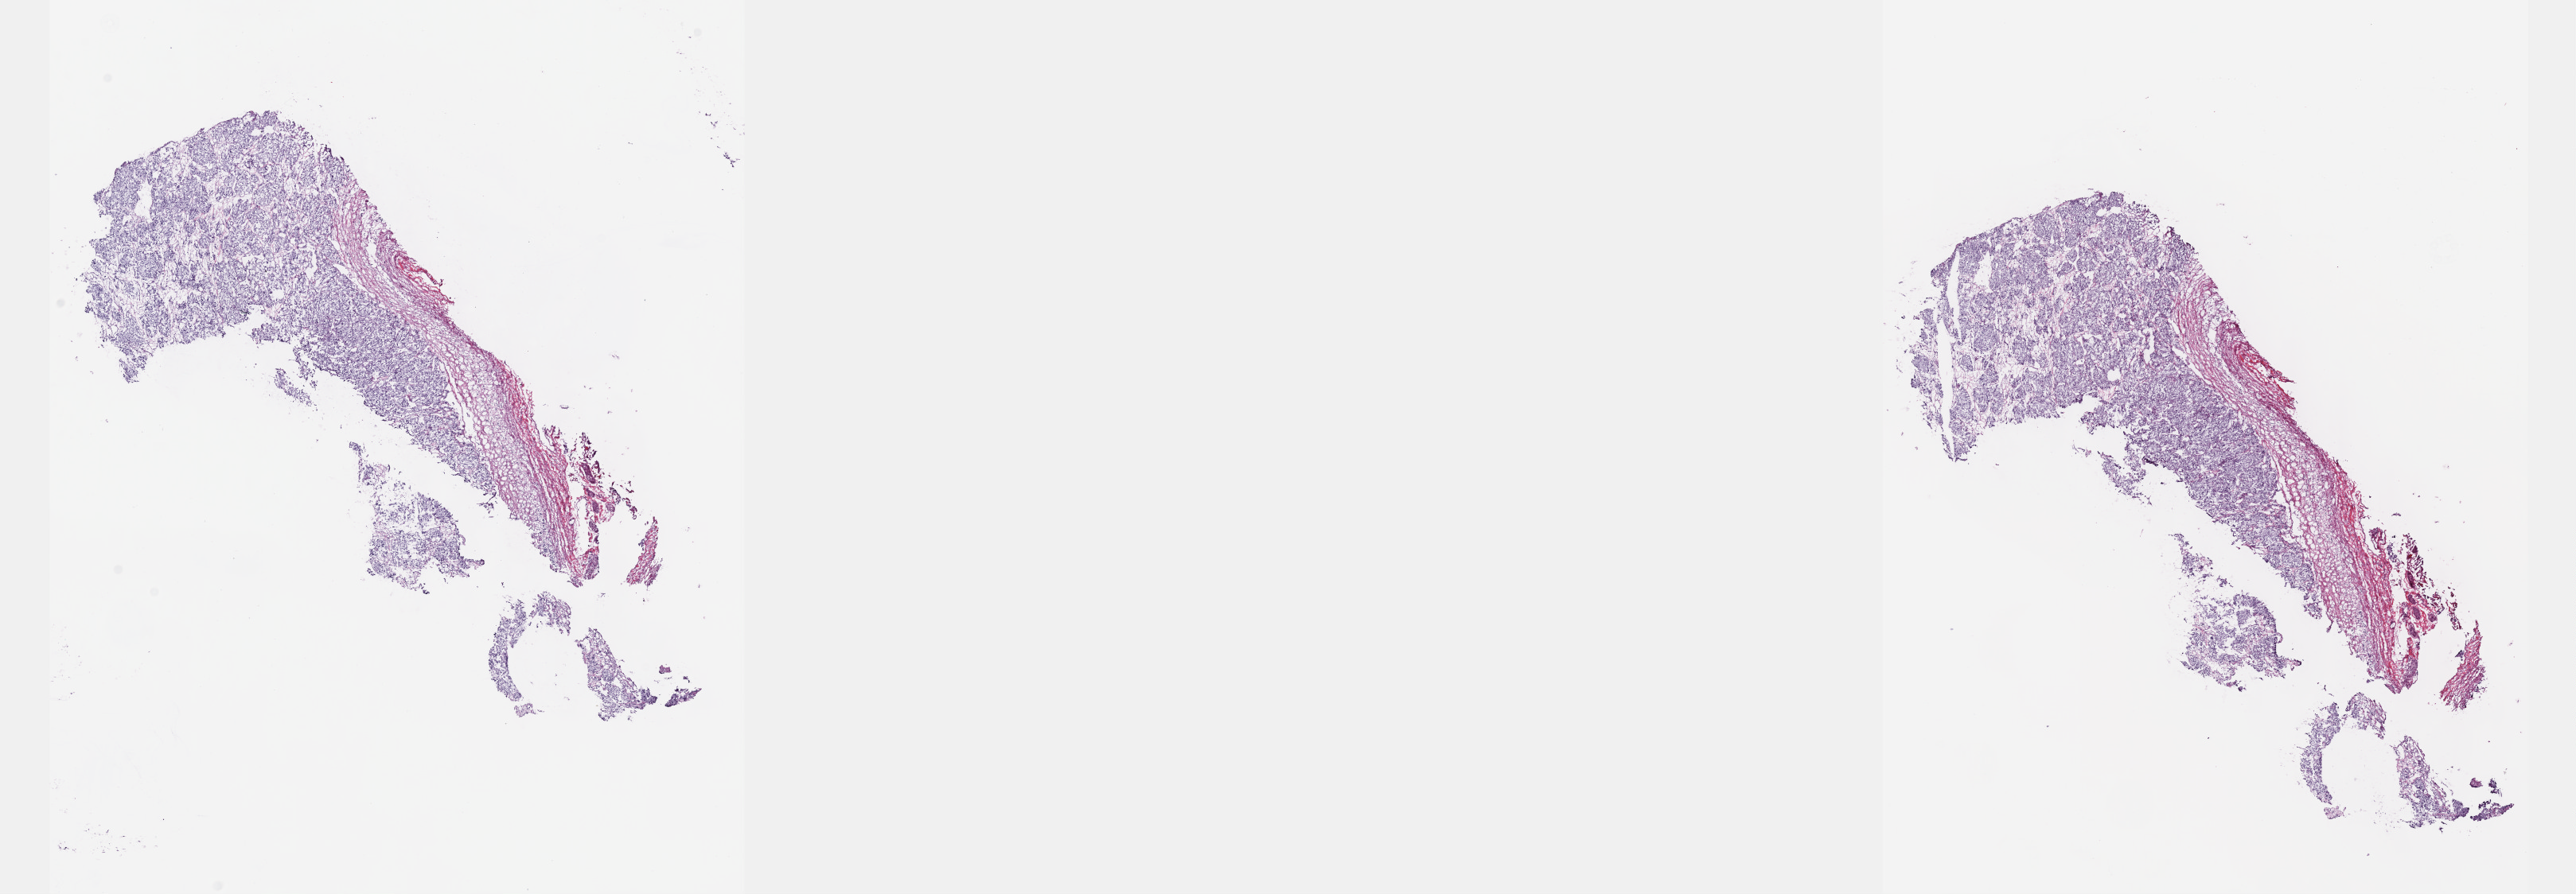
H&E whole-slide image — shown as a low-resolution overview of the whole scanned area (about 26.2 x 9.1 mm, from a 40x scan); frozen section from the top of the tissue portion; adrenal gland, primary tumour sample. Female patient; age at initial diagnosis 25 years. Slide review estimates, as recorded: tumour cells 90%, tumour nuclei 98%, normal cells 0%, stromal cells 10%, necrosis 0%. Inflammatory infiltration, as recorded: lymphocyte infiltration 0%, monocyte infiltration 0%, neutrophil infiltration 0%.
- pathologic diagnosis: Pheochromocytoma, NOS